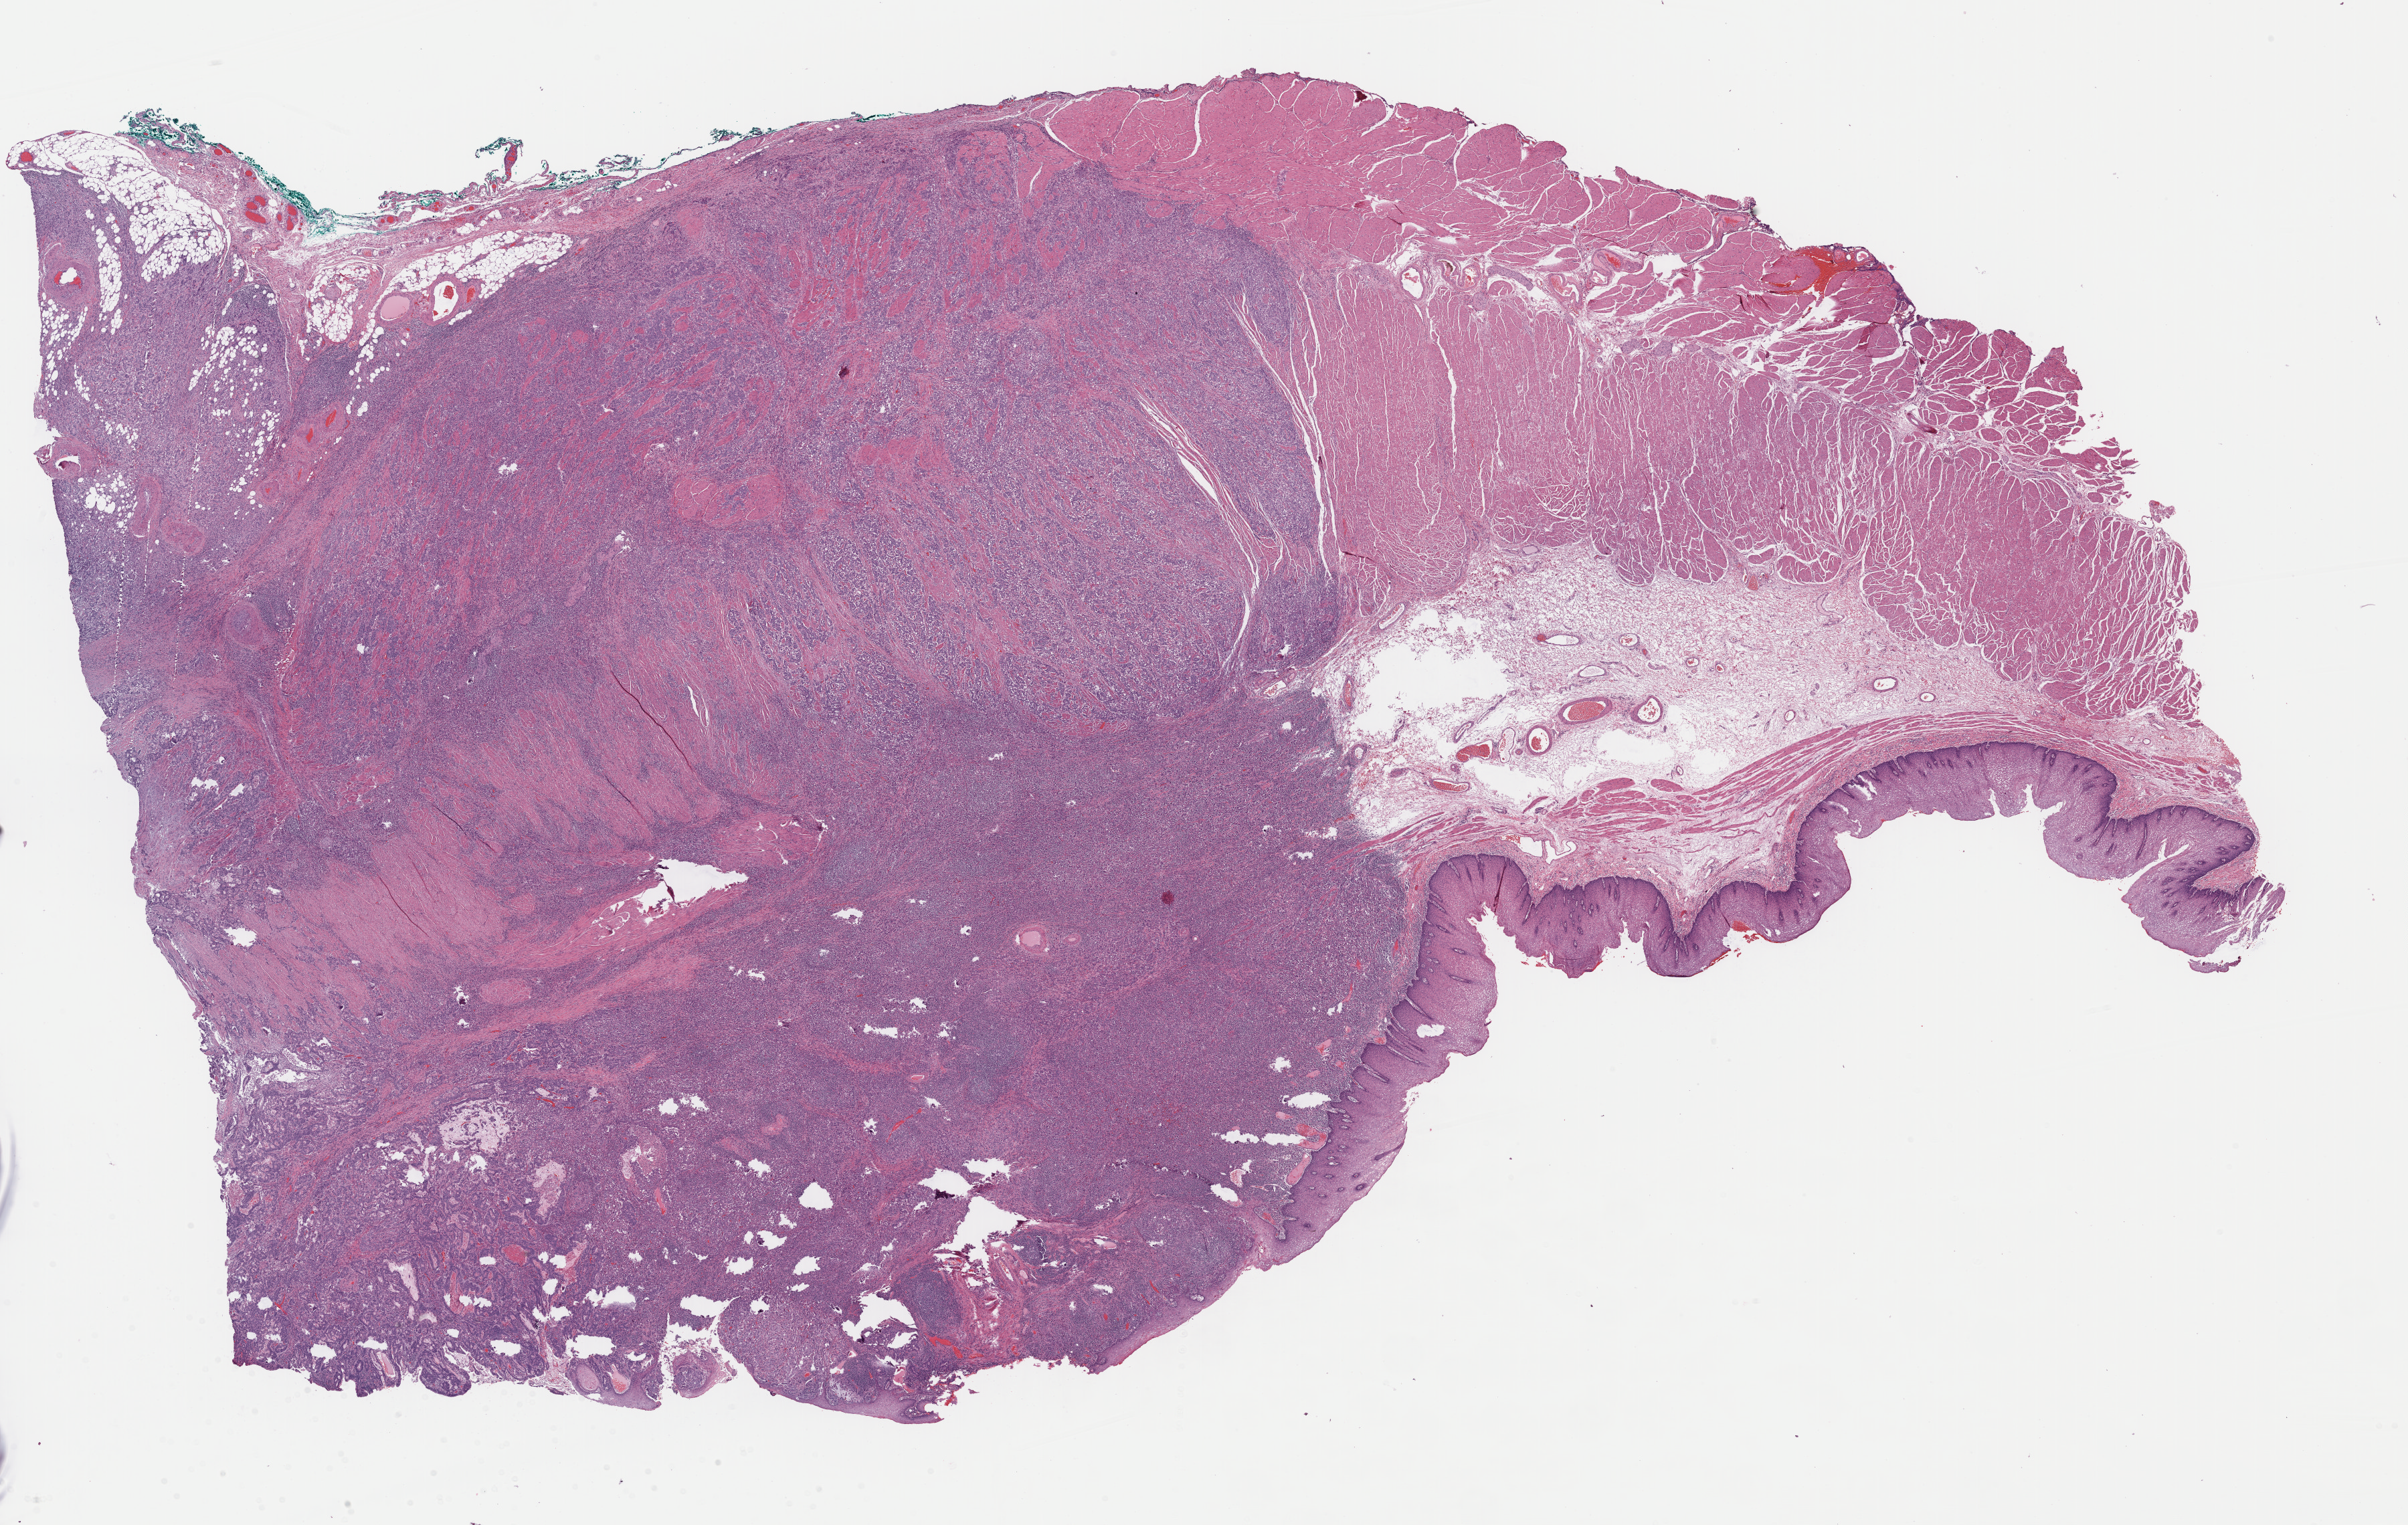
Whole-slide histology image, Hematoxylin and eosin (H&E) stained, a low-resolution overview of the entire scanned area, about 28.4 x 18.0 mm (slide scanned at 40x). FFPE section. Esophagus, primary tumour sample. Patient: male, age at initial diagnosis 81 years. Histologic grade: G2 (moderately differentiated).
* lymph nodes positive (case pathology): 3 of 17 examined
* pathologic diagnosis: Adenocarcinoma, NOS (lower third of esophagus)
* AJCC pathologic stage: IIIB